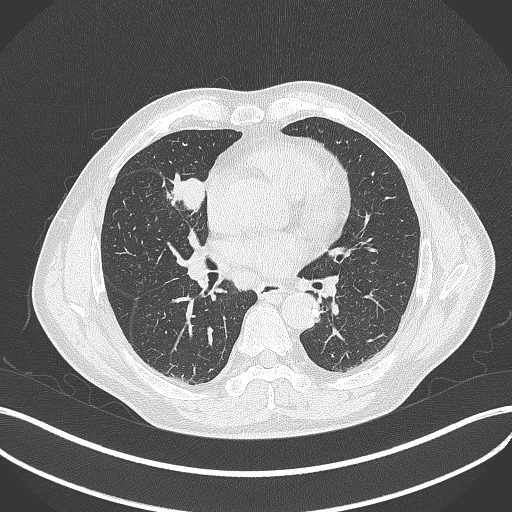
Chest CT, one axial slice; slice 199 of 429 in the series (ordered by position); reconstruction kernel B70f; lung window (W 1500 / L -600 HU); 1 mm slice thickness; 512 × 512 image matrix. Patient: male, 61 years. Case-level facts recorded for this patient, not image findings: clinical TNM (as recorded): T2b N1 M0.
Outlined on this slice (bounding box drawn by a radiologist):
- lung tumour (recorded histology: squamous cell carcinoma): box from (x=168, y=169) to (x=209, y=221) px